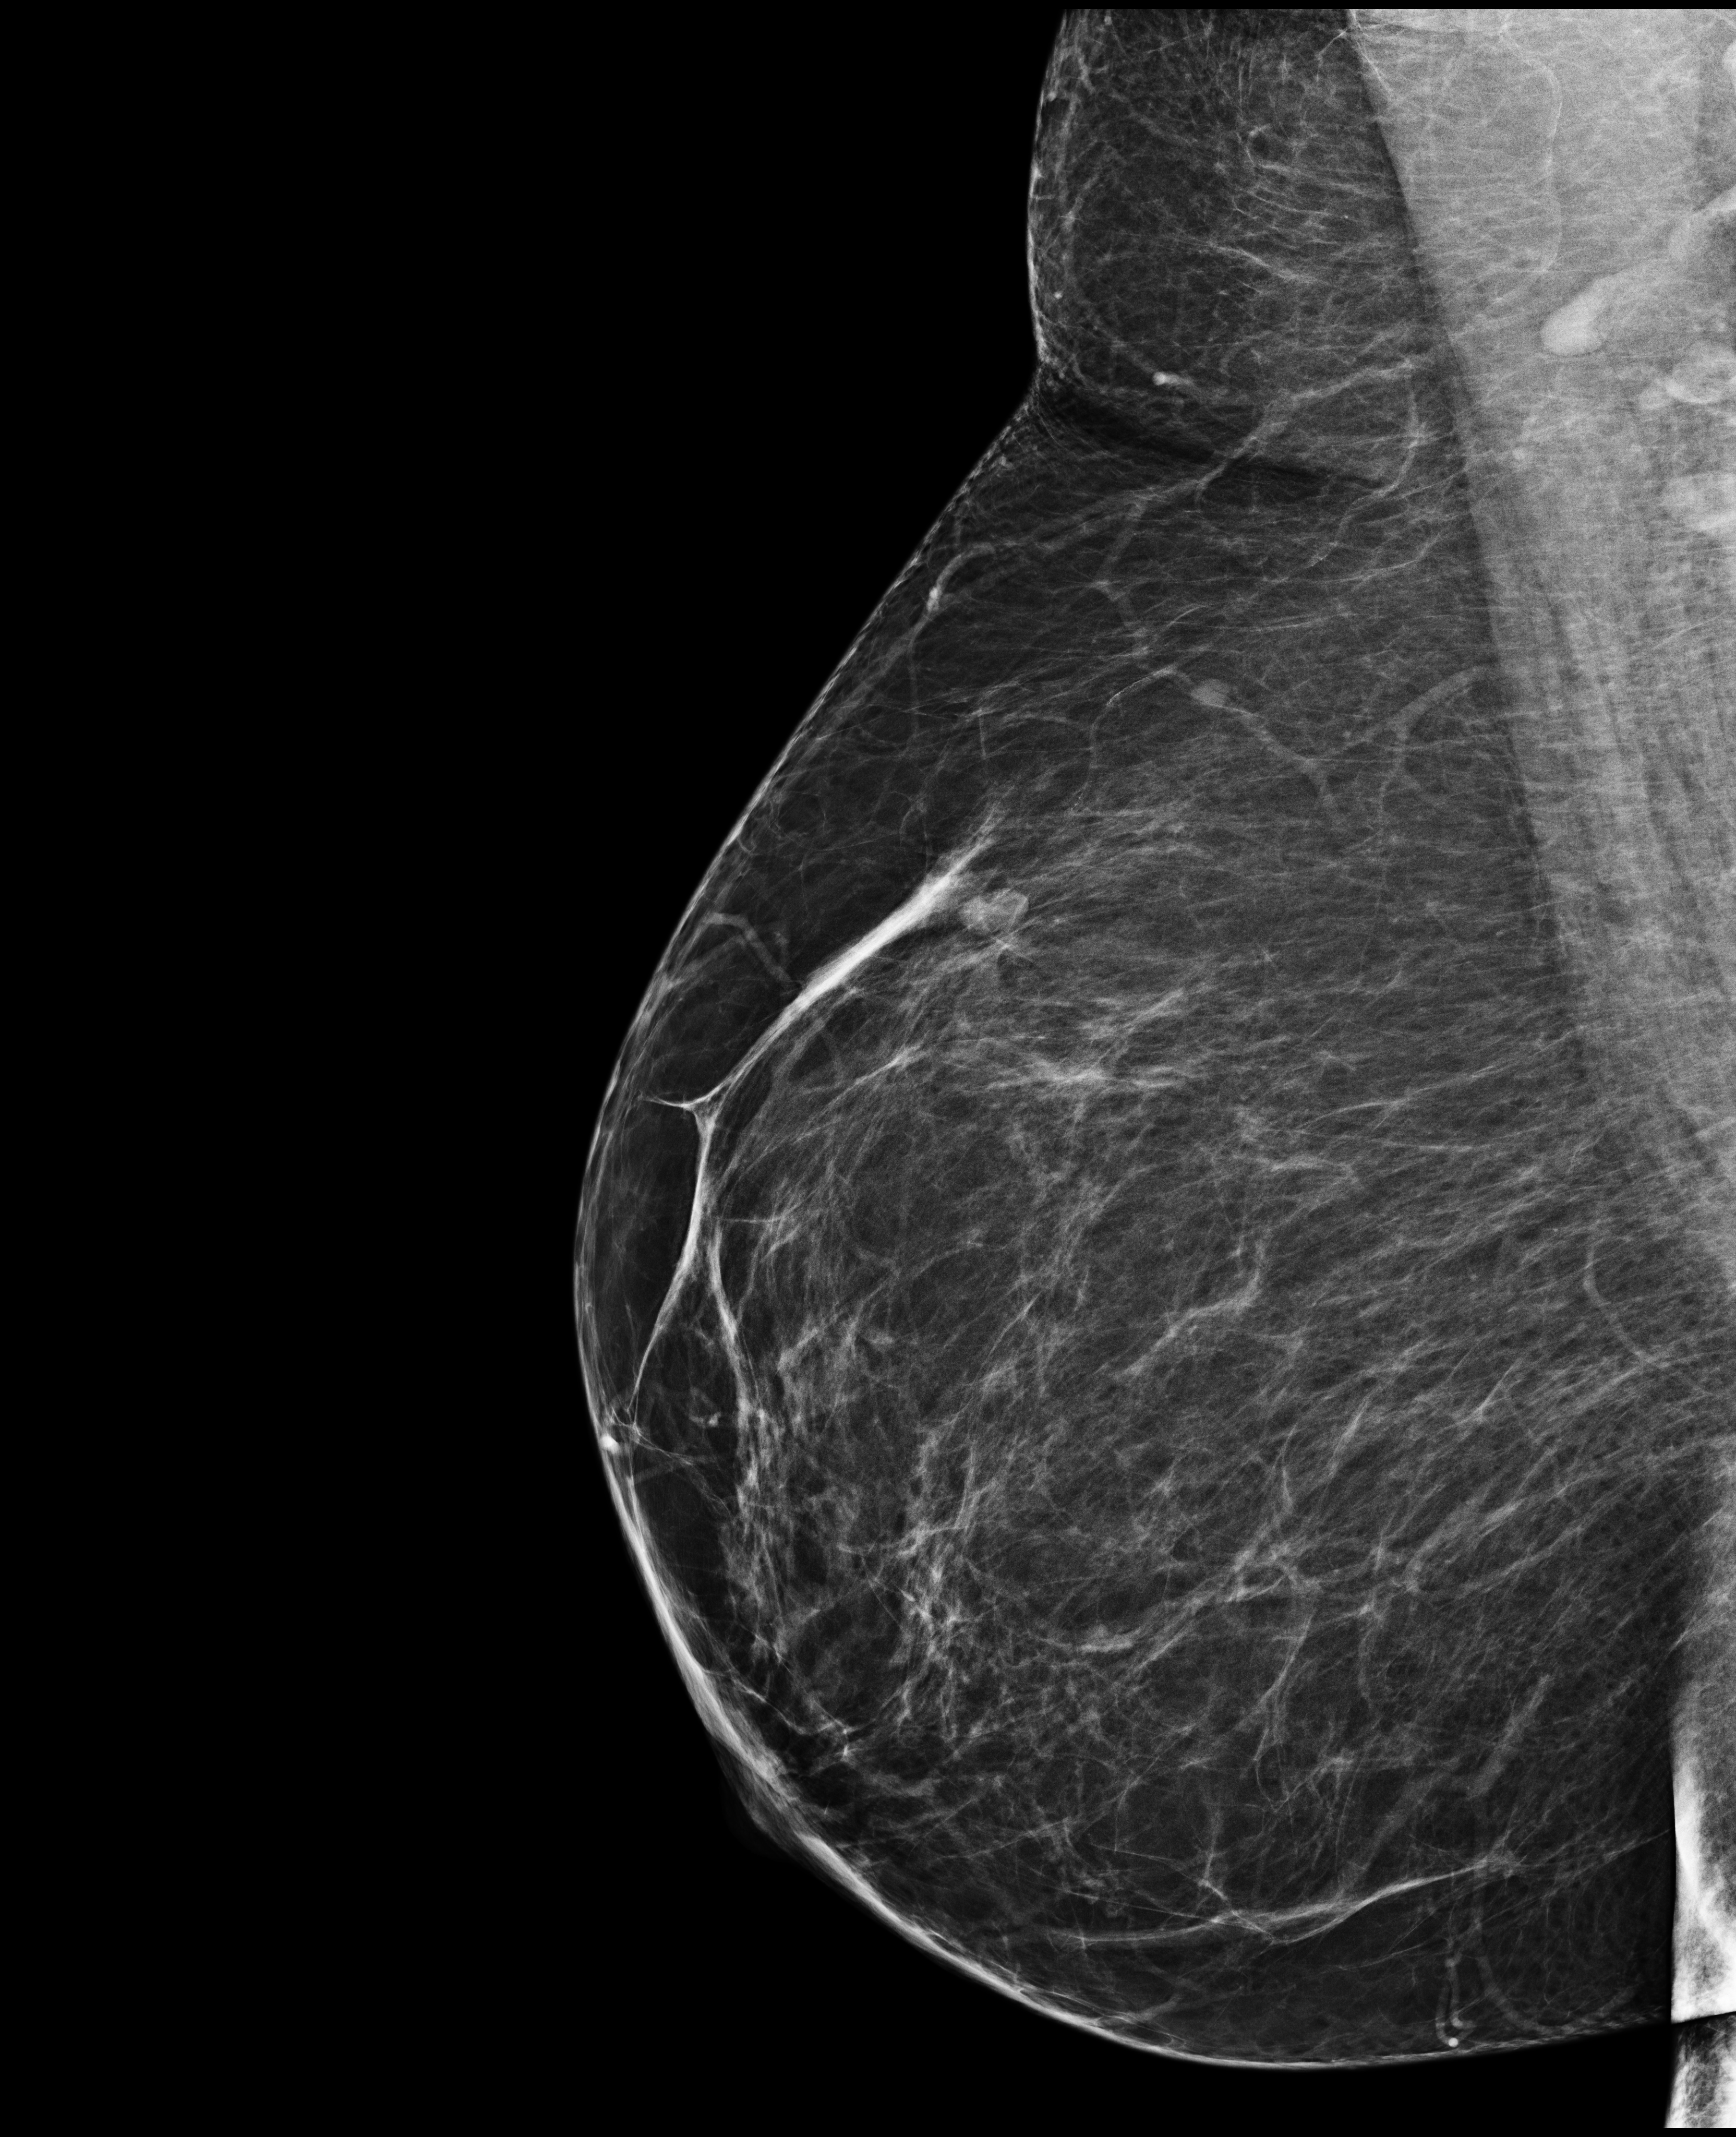
Screening examination. Patient: female, 52 years.
Image type: full-field digital mammogram. Breast: right. Projection: mediolateral oblique (MLO) view.